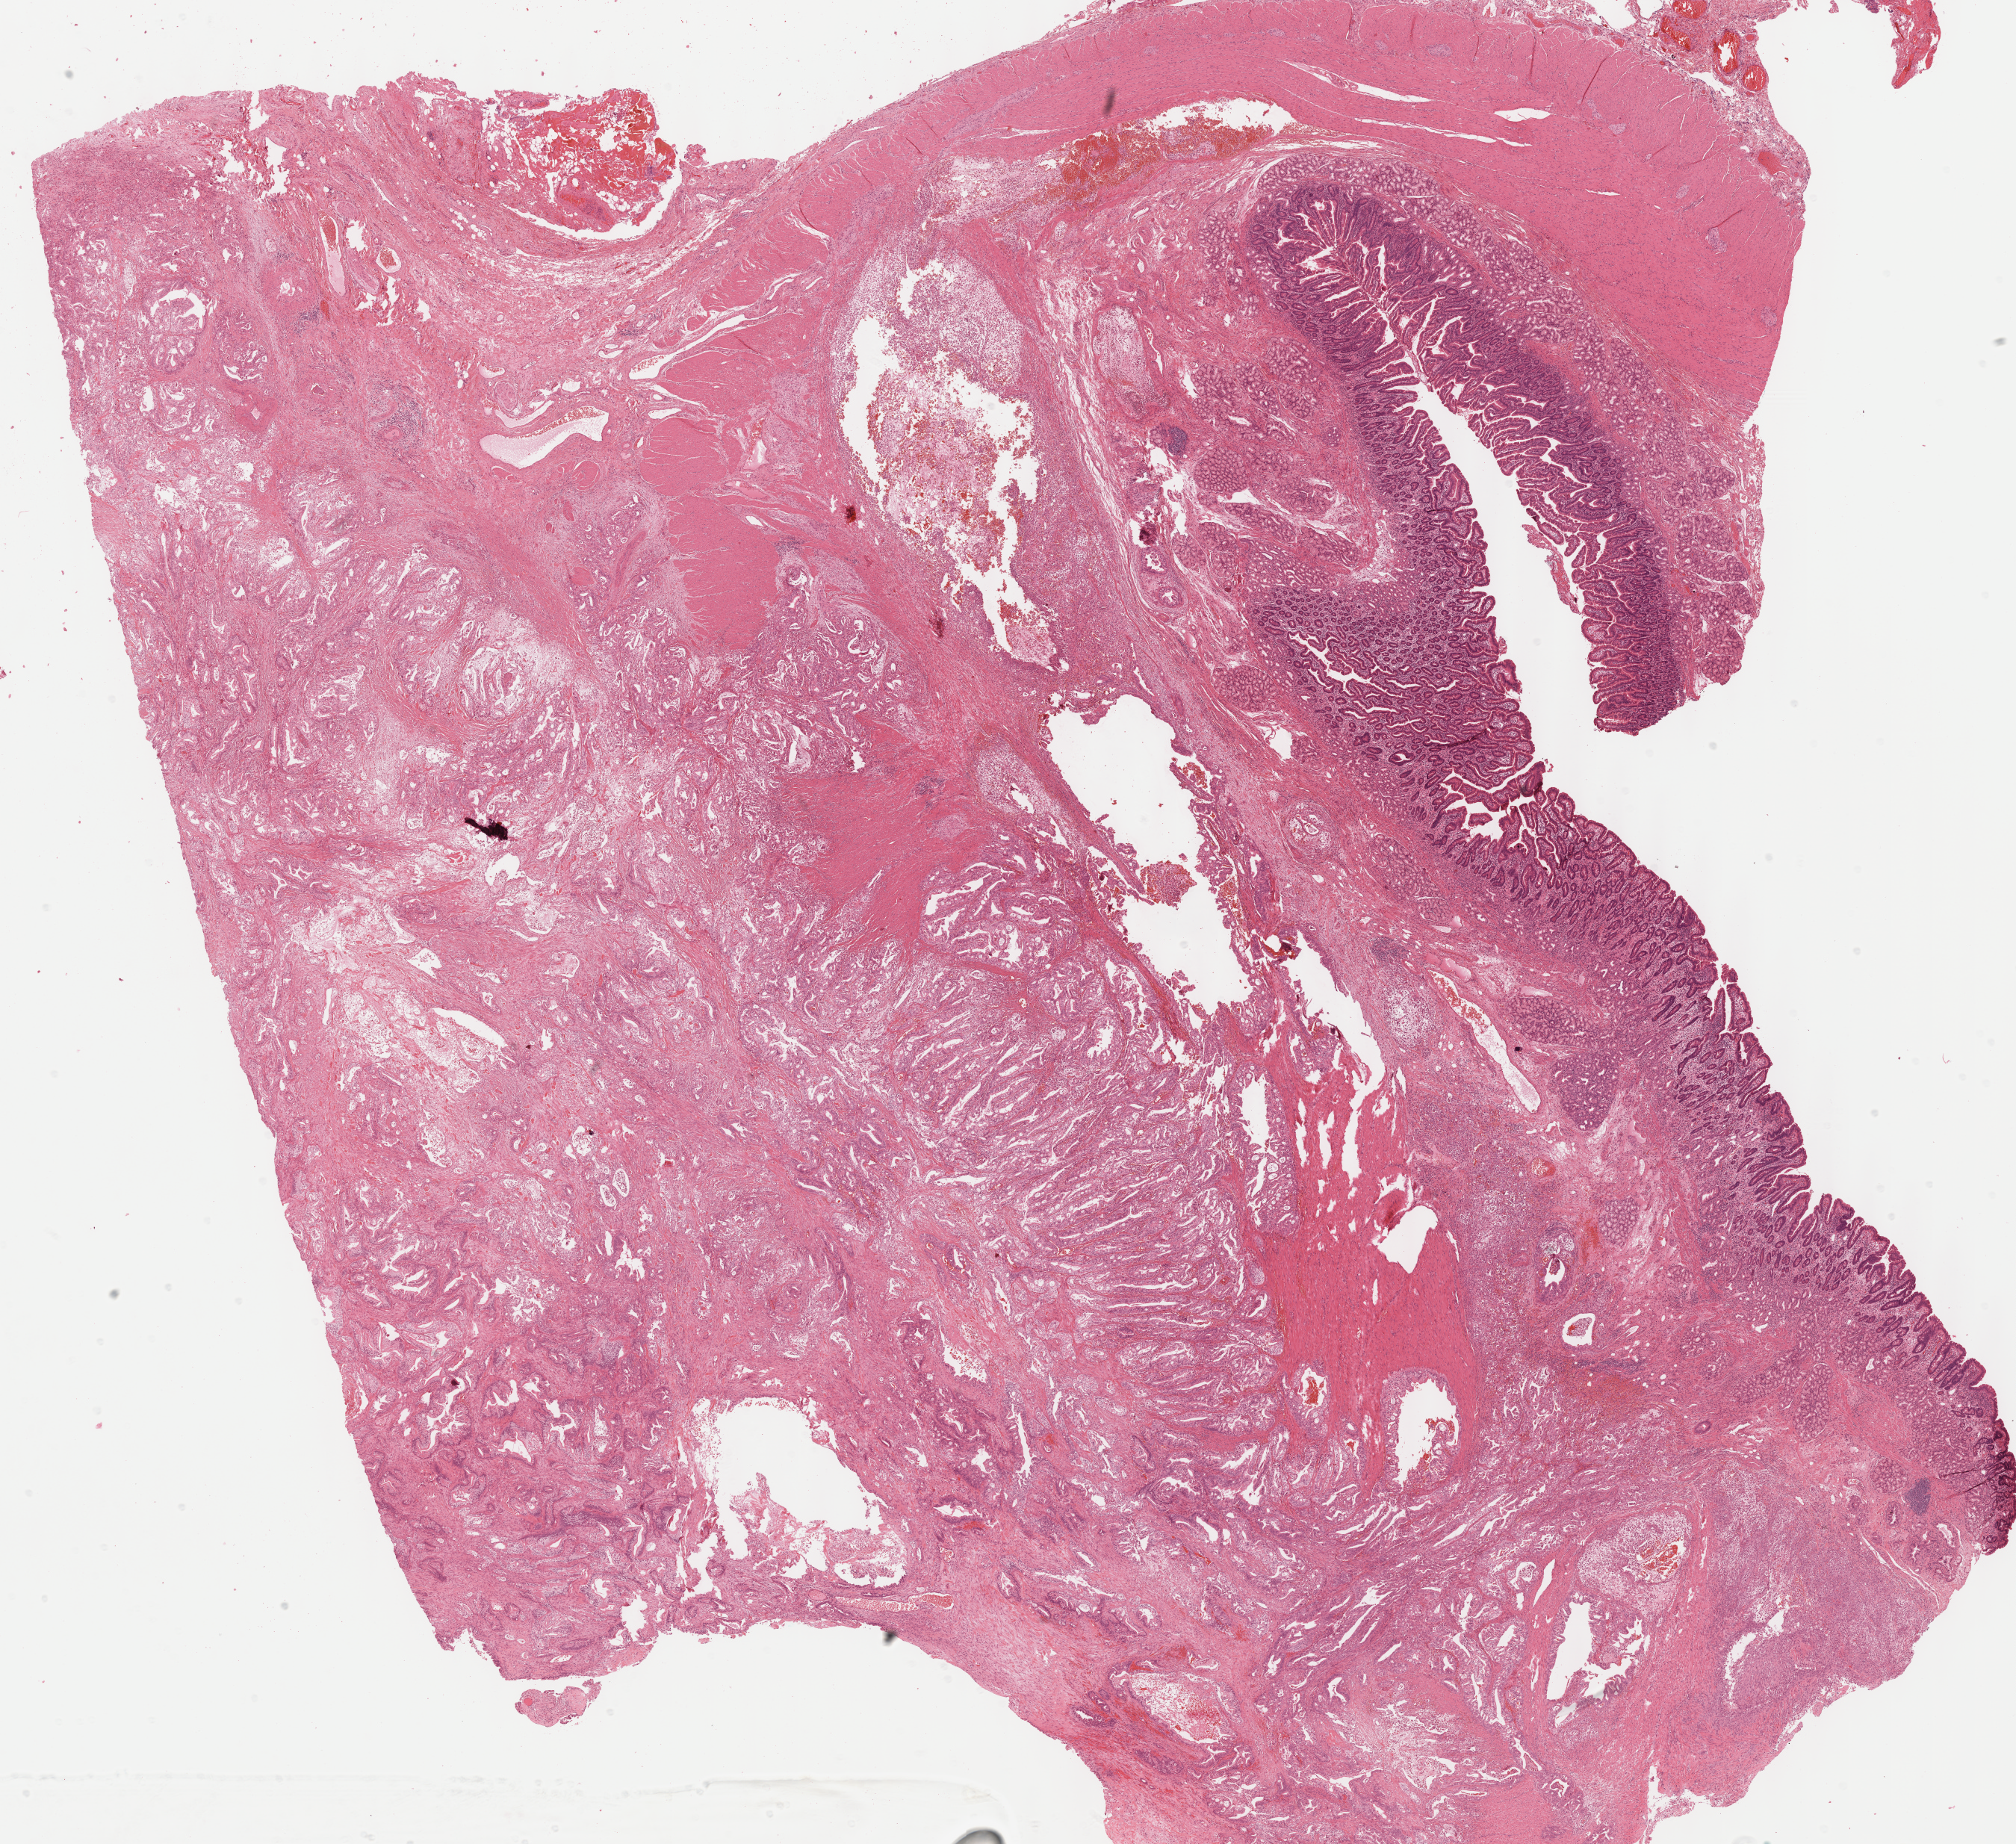
Whole-slide histology image, Hematoxylin and eosin (H&E) stained — shown as a low-resolution overview of the whole scanned area (about 21.5 x 19.6 mm, from a 40x scan); formalin-fixed paraffin-embedded (FFPE) diagnostic section; pancreas, primary tumour sample. Male, age 76 years at initial diagnosis. Histologic grade: G2 (moderately differentiated).
Histologic diagnosis: Infiltrating duct carcinoma, NOS. Lymph nodes positive (case pathology): 6 of 21 examined. AJCC pathologic stage: IIB (7th edition).